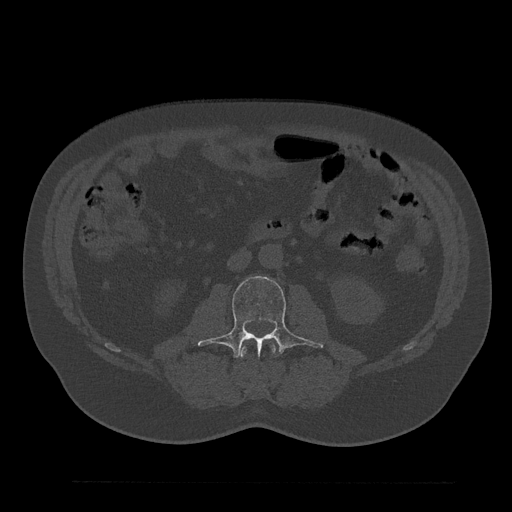
CT including the spine, one axial slice. Slice 45 of 797 in the series (ordered by position). 120 kVp. Bone window (W 1800 / L 400 HU). 512 × 512 image matrix, field of view 430 × 430 mm. Patient: male, 61 years. From the clinical record (not read from this slice): primary cancer: prostate.
Structures marked on this image (semi-automatic segmentation, software-assisted and operator-edited):
- L2 vertebra: bounding box [x1, y1, x2, y2] px = [240, 344, 276, 358]
- L3 vertebra: [198, 276, 323, 359]